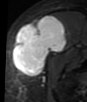
MRI of an extremity soft-tissue mass, one axial slice; slice 24 of 48 in the series (ordered by position); STIR; MR volume resampled by the dataset authors to the PET/CT grid (not the native acquisition matrix); 87 × 102 image matrix, field of view 85 × 100 mm. Female patient. Case-level facts recorded for this patient, not image findings: histological type: synovial sarcoma; grade: intermediate; site of the primary tumour: right thigh.
Outlined on this slice (expert contour drawn on MRI and transferred to this co-registered scan by the dataset authors):
- gross tumour volume including surrounding oedema: box from (x=13, y=15) to (x=68, y=76) px
- gross tumour volume (mass): (x=13, y=15)–(x=68, y=76)